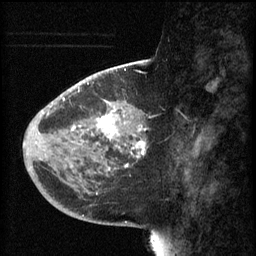
Breast MRI (dynamic contrast-enhanced), one sagittal slice; slice 23 of 60 in the series (ordered by position); 3 images stored at this slice position (order not interpretable as contrast timing); 1.5 T; TE 4.2 ms, TR 8.1 ms; 2 mm slice thickness; 256 × 256 image matrix, field of view 200 × 200 mm. Female patient, age 44 years.
Annotated regions visible in this slice (semi-automatically segmented with operator editing):
- analysis volume of interest (the breast-tissue region the enhancement analysis was run in; not a lesion): bounding box (x1, y1, x2, y2) in pixels: (59, 110, 149, 169)
- tumour enhancement mask (voxels above the 70 % enhancement threshold inside the analysis volume of interest): (72, 110, 146, 169)